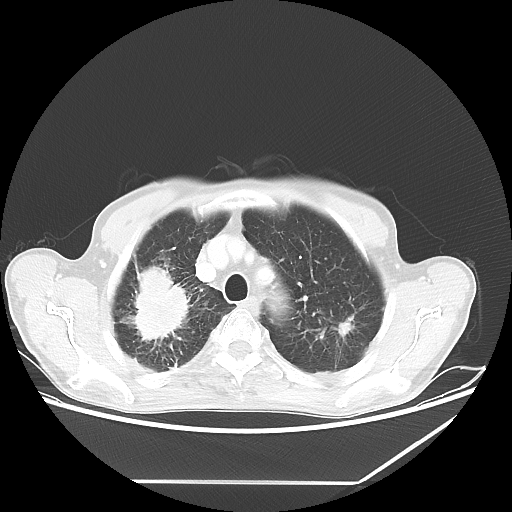
Chest CT, one axial slice. Position 51 of 65 along the scan axis. Reconstruction kernel LUNG. Lung window (W 1500 / L -600 HU). 5 mm slice thickness. 512 × 512 image matrix. Male patient, age 68 years. From the clinical record (not read from this slice): clinical TNM (as recorded): T3 N3 M0.
Structures marked on this image (bounding box drawn by a radiologist):
- lung tumour (recorded histology: adenocarcinoma): bounding box <110,259,192,356> (left, top, right, bottom; pixels)